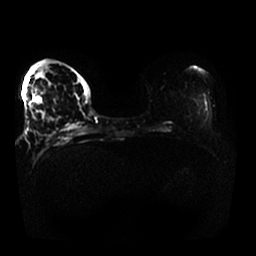
Breast MRI, one axial slice. Slice 11 of 25 in the series (ordered by position). Diffusion-weighted series; image 2 of 4 stored at this slice position (different b-values; order by instance number). 1.5 T. 4 mm slice thickness. 256 × 256 image matrix, field of view 370 × 370 mm. Female patient.
Structures marked on this image (expert manual segmentation):
- tumour on diffusion-weighted imaging: bounding box [x1, y1, x2, y2] px = [34, 64, 51, 121]